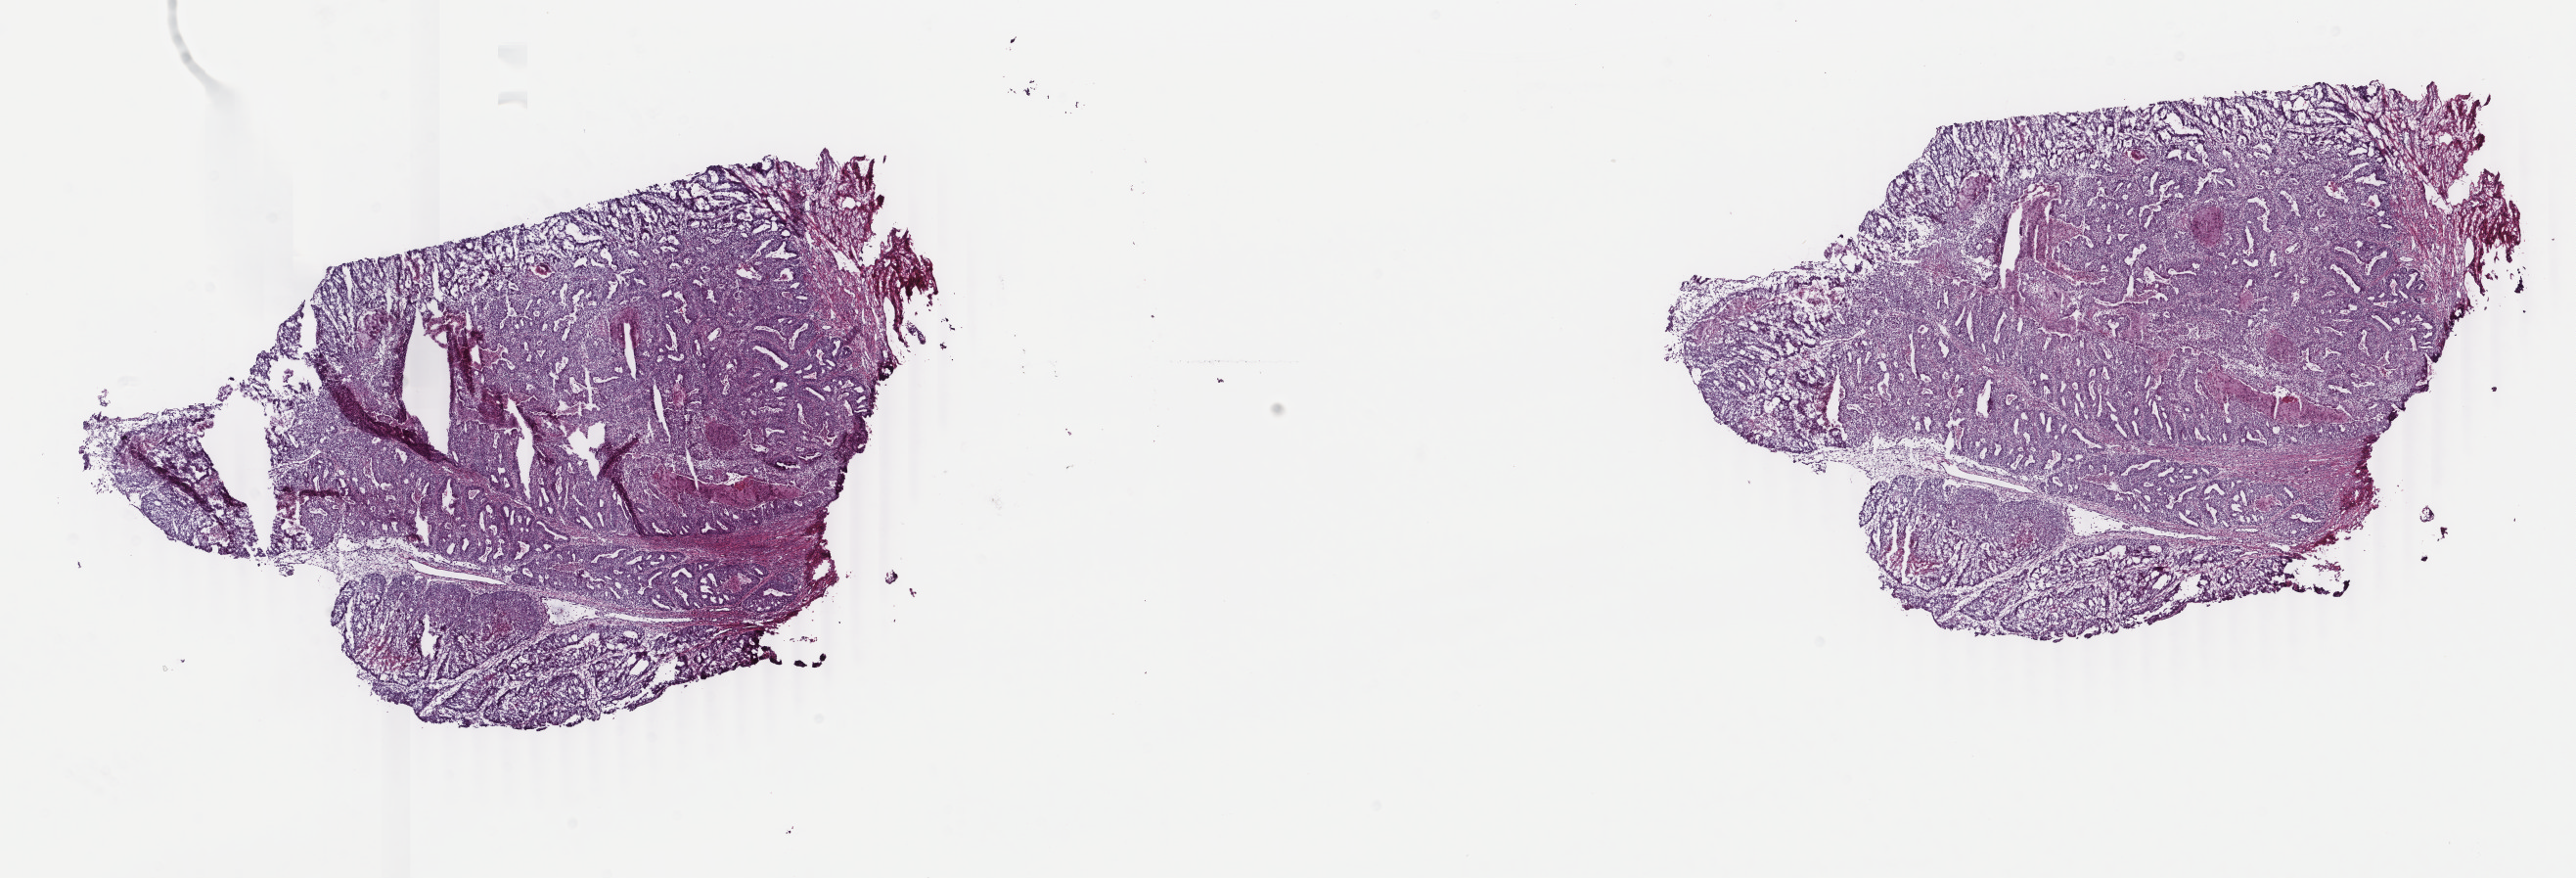
Digitized H&E tissue section (whole slide), shown as a low-resolution overview of the whole scanned area (about 20.9 x 7.1 mm), frozen section, primary tumour sample from the uterus. Patient: female, age at initial diagnosis 84 years. Histologic grade: G2 (moderately differentiated). Composition of this section per pathologist review: tumour cells 70%, tumour nuclei 70%, normal cells 0%, stromal cells 20%, necrosis 10%. Infiltration values recorded for this section: lymphocyte infiltration 40%, monocyte infiltration 20%, neutrophil infiltration 20%.
FIGO stage: IA. Pathologic diagnosis: Endometrioid adenocarcinoma, NOS.